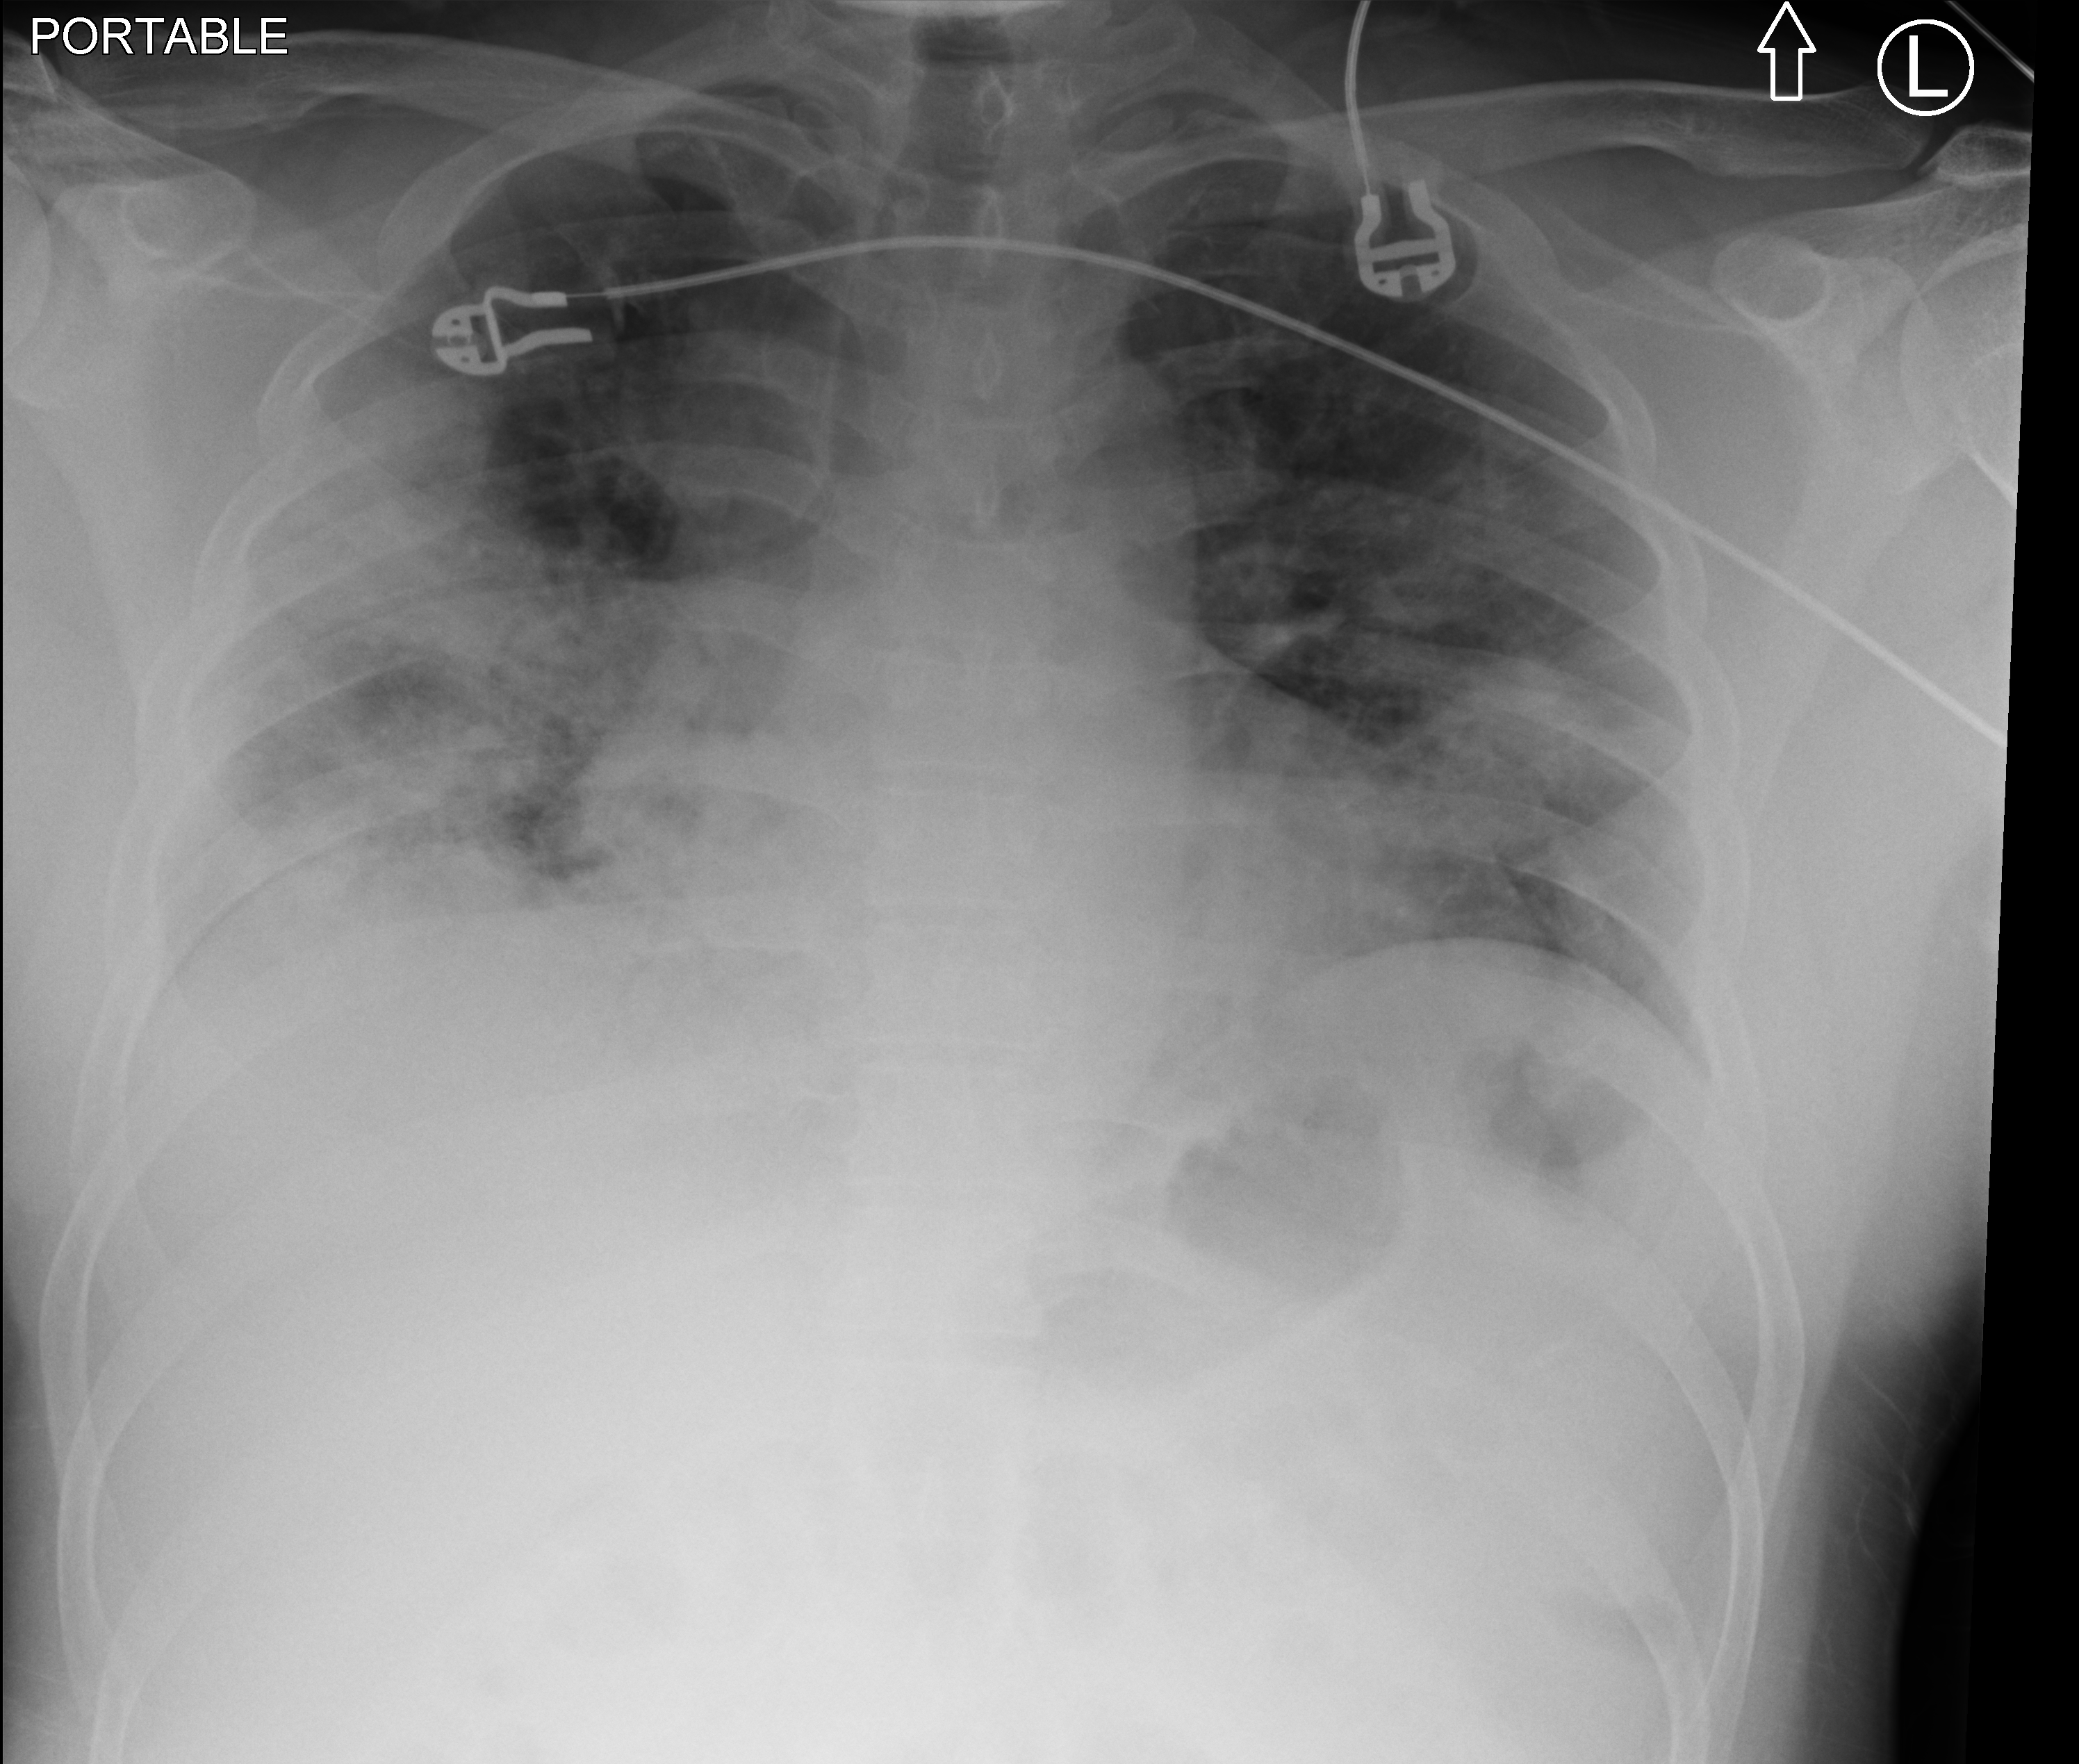
Chest X-ray (portable); anteroposterior (AP) projection. Patient hospitalised with COVID-19; male, aged 18–59 years.
From the hospital-stay record, not from the radiograph (when in the stay this image was taken is not recorded): admitted to intensive care during this hospital stay: no; mechanically ventilated during this hospital stay: no; hypertension (admission record): no.